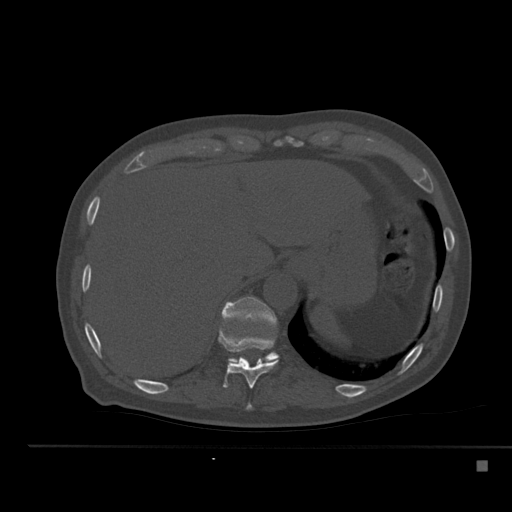
CT including the spine, one axial slice; slice 264 of 517 in the series (ordered by position); bone window (W 1800 / L 400 HU); 1.5 mm slice thickness; 512 × 512 image matrix. Patient: male, 70 years. From the clinical record (not read from this slice): primary cancer: renal.
Structures marked on this image (semi-automatic segmentation, software-assisted and operator-edited):
- T10 vertebra: bounding box [x1, y1, x2, y2] px = [218, 329, 279, 389]
- T11 vertebra: [221, 297, 279, 363]
- T9 vertebra: [246, 403, 253, 410]